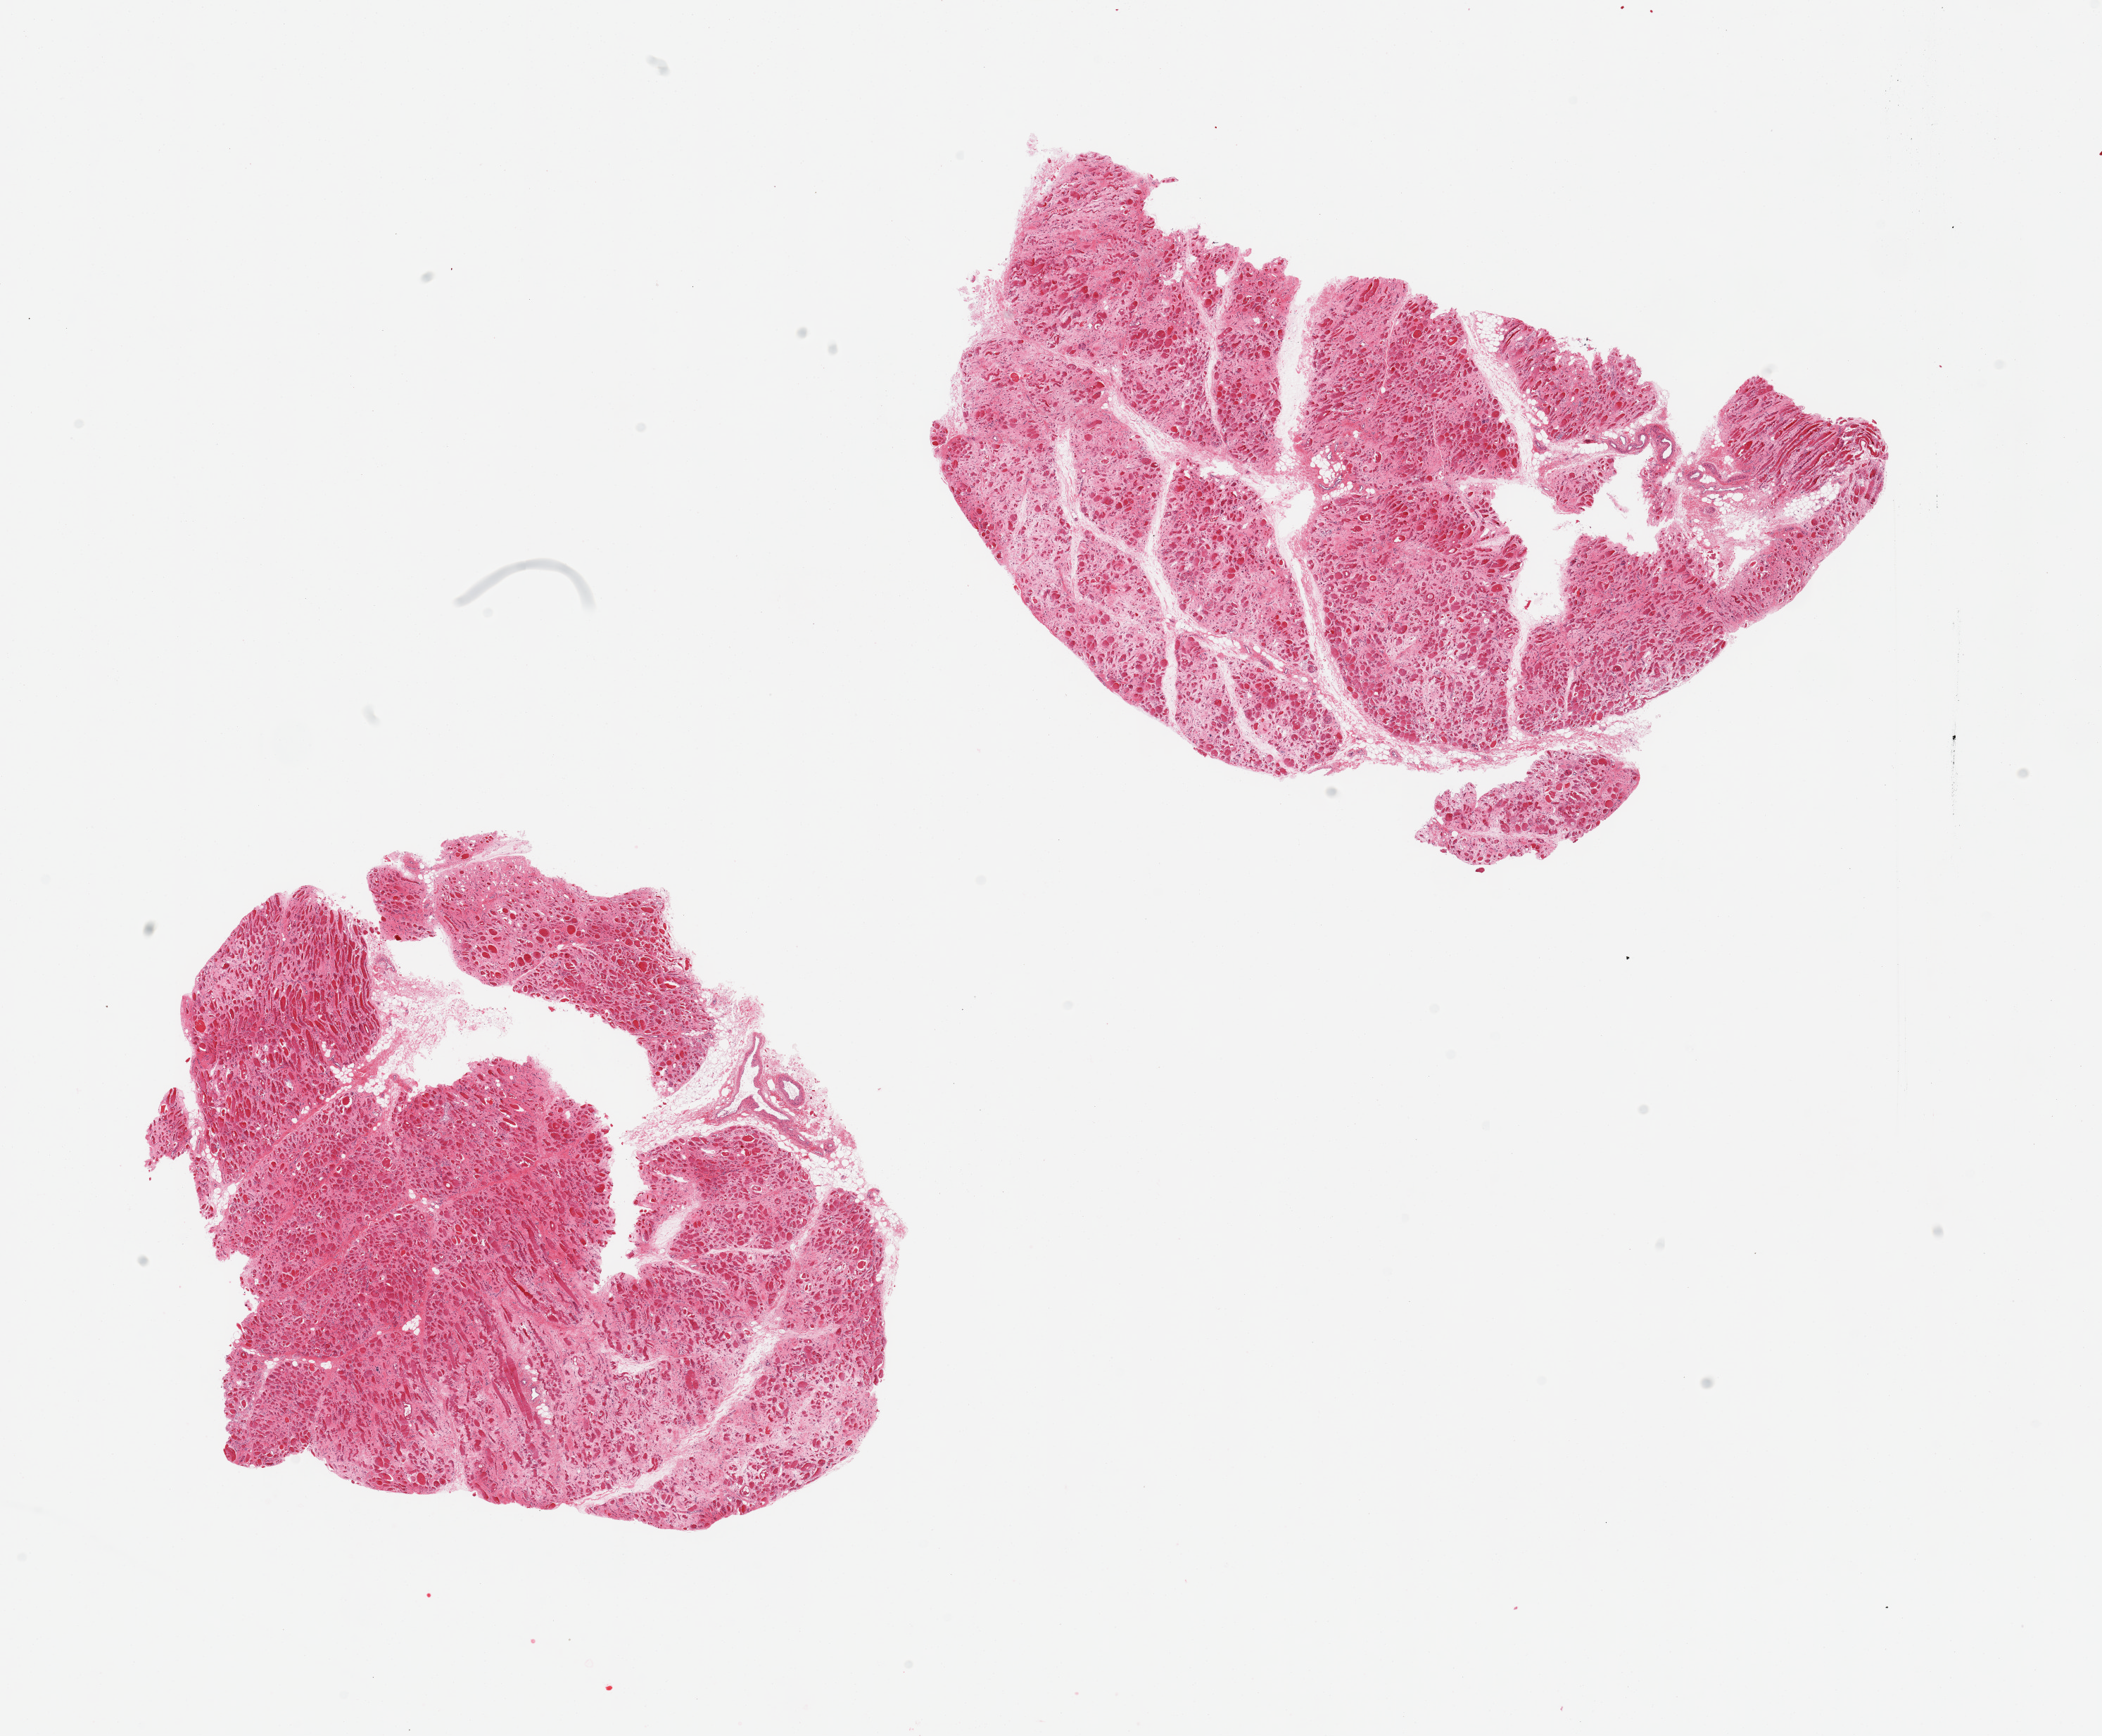
Hematoxylin and eosin (H&E) whole-slide image — shown as a low-resolution overview of the whole scanned area (about 23.6 x 19.5 mm), PAXgene-fixed, paraffin-embedded tissue, sampled site (target tissue): skeletal muscle, tissue donor sample. Male donor.
Reviewer comment on this tissue sample: 2 pieces, markedly atrophic, ~50% interstitial fibrous tissue; fibres abnormal.